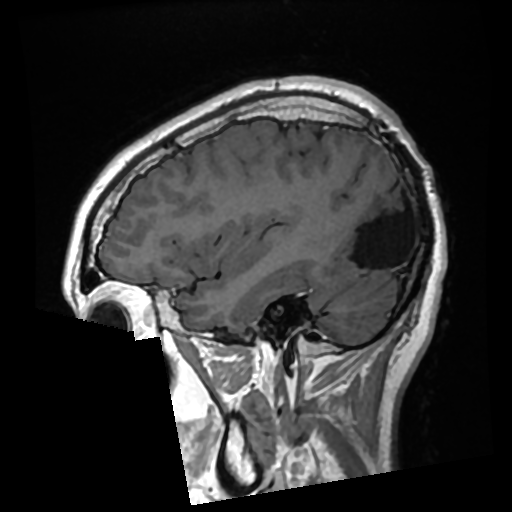
Brain MRI from a brain-tumour surgery series, one sagittal slice; position 86 of 276 along the scan axis; T1-weighted post-contrast; 0.7 mm slice thickness; 512 × 512 image matrix, field of view 250 × 250 mm. From the clinical record (not read from this slice): histopathology: Glioma with ependymal features; WHO grade: 2; tumour location: Left Parietal.
Outlined on this slice (outlined manually by an expert reader):
- previous resection cavity: bounding box (x1, y1, x2, y2) in pixels: (338, 182, 408, 268)